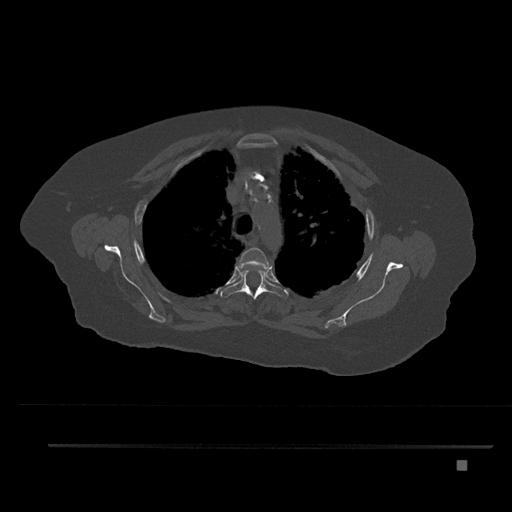
CT including the spine, one axial slice; slice 613 of 797 in the series (ordered by position); reconstruction kernel Br40s/3; 120 kVp; bone window (W 1800 / L 400 HU); 512 × 512 image matrix, field of view 437 × 437 mm. Patient: female, 76 years. Case-level facts recorded for this patient, not image findings: primary cancer: lung.
Outlined on this slice (semi-automatic segmentation, software-assisted and operator-edited):
- T3 vertebra: bounding box (x1, y1, x2, y2) in pixels: (238, 247, 271, 270)
- T4 vertebra: (220, 263, 289, 299)